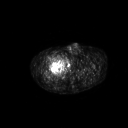
FDG PET of an extremity soft-tissue mass (from a PET/CT study), one axial slice. Position 285 of 311 along the scan axis. 3.27 mm slice thickness. 128 × 128 image matrix, field of view 700 × 700 mm. Male patient, age 50 years. Case-level facts recorded for this patient, not image findings: histological type: undifferentiated - pleiomorphic; grade: high; site of the primary tumour: right thigh.
Structures marked on this image (expert contour drawn on MRI and transferred to this co-registered scan by the dataset authors):
- gross tumour volume including surrounding oedema: bounding box [x1, y1, x2, y2] px = [52, 54, 65, 67]
- gross tumour volume (mass): [52, 55, 64, 66]